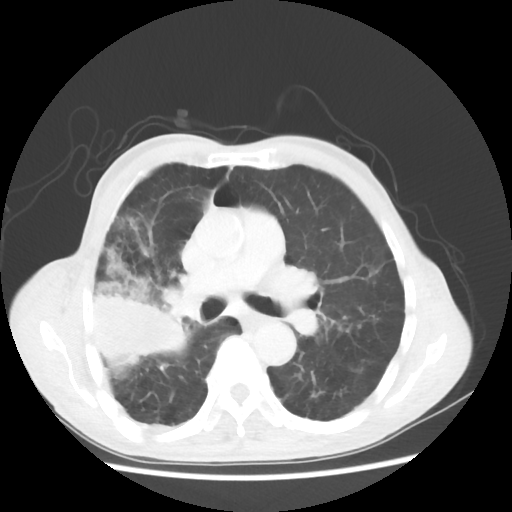
Chest CT, one axial slice. Slice 31 of 58 in the series (ordered by position). Reconstruction kernel STANDARD. 100 kVp. Lung window (W 1500 / L -600 HU). 512 × 512 image matrix, field of view 351 × 351 mm. Patient: male, 75 years. Case-level facts recorded for this patient, not image findings: clinical TNM (as recorded): T4 N1 M1.
Structures marked on this image (bounding box drawn by a radiologist):
- lung tumour (recorded histology: adenocarcinoma): bounding box (x1, y1, x2, y2) in pixels: (89, 271, 190, 375)